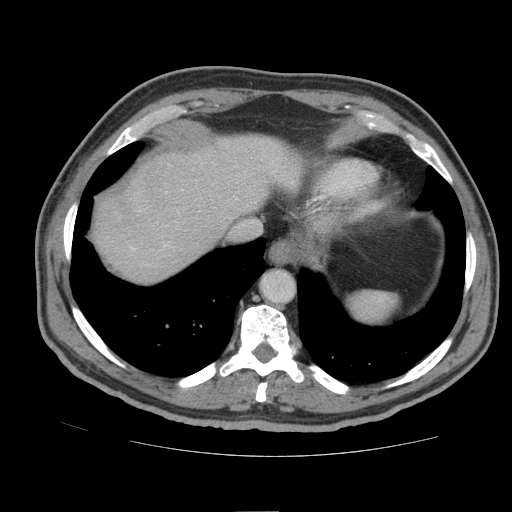
Contrast-enhanced abdominal CT (liver protocol), one axial slice; position 76 of 105 along the scan axis; 140 kVp; soft-tissue window (W 400 / L 40 HU); 2.5 mm slice thickness; 512 × 512 image matrix, field of view 380 × 380 mm. Case-level facts recorded for this patient, not image findings: diagnosis: hepatocellular carcinoma (patient treated with transarterial chemoembolisation; whether this scan precedes or follows treatment is not stated here); TNM stage (as recorded): Stage-IIIB.
Outlined on this slice (semi-automatically segmented with operator editing):
- abdominal aorta: box from (x=262, y=271) to (x=294, y=302) px
- liver parenchyma outside the tumour (the mass and vessels are separate outlines, so this box may not span the whole liver): (x=94, y=134)–(x=300, y=282)